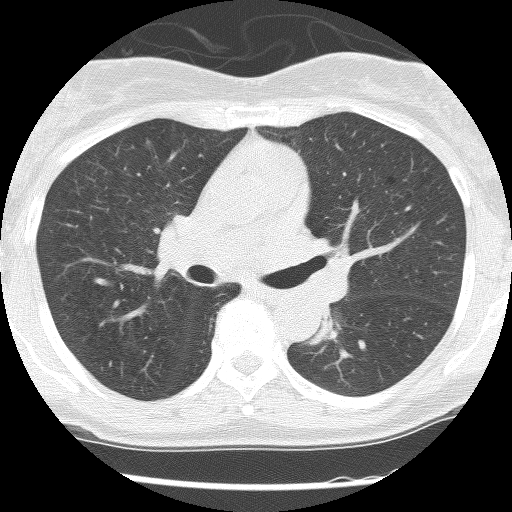
Axial slice from a low-dose chest CT screening exam. Second screening round (one year after baseline). Lung window (W 1500 / L -600 HU). 2.5 mm slice thickness. Female, age 62 years at enrolment.
• Lesion marked by an expert reader, bounding box (x1, y1, x2, y2) in pixels: (299, 303, 351, 351).
• Screening reader's record for this exam (one nodule recorded; not confirmed to be the boxed lesion): non-calcified nodule or mass ≥4 mm, right upper lobe, 30 × 30 mm, poorly defined margins, ground glass attenuation, pre-existing on the prior screen: yes; interval growth: no.
• Note: the box lies in the patient's left hemithorax on this image, whereas the reader's record names the right lung; they may be different findings.